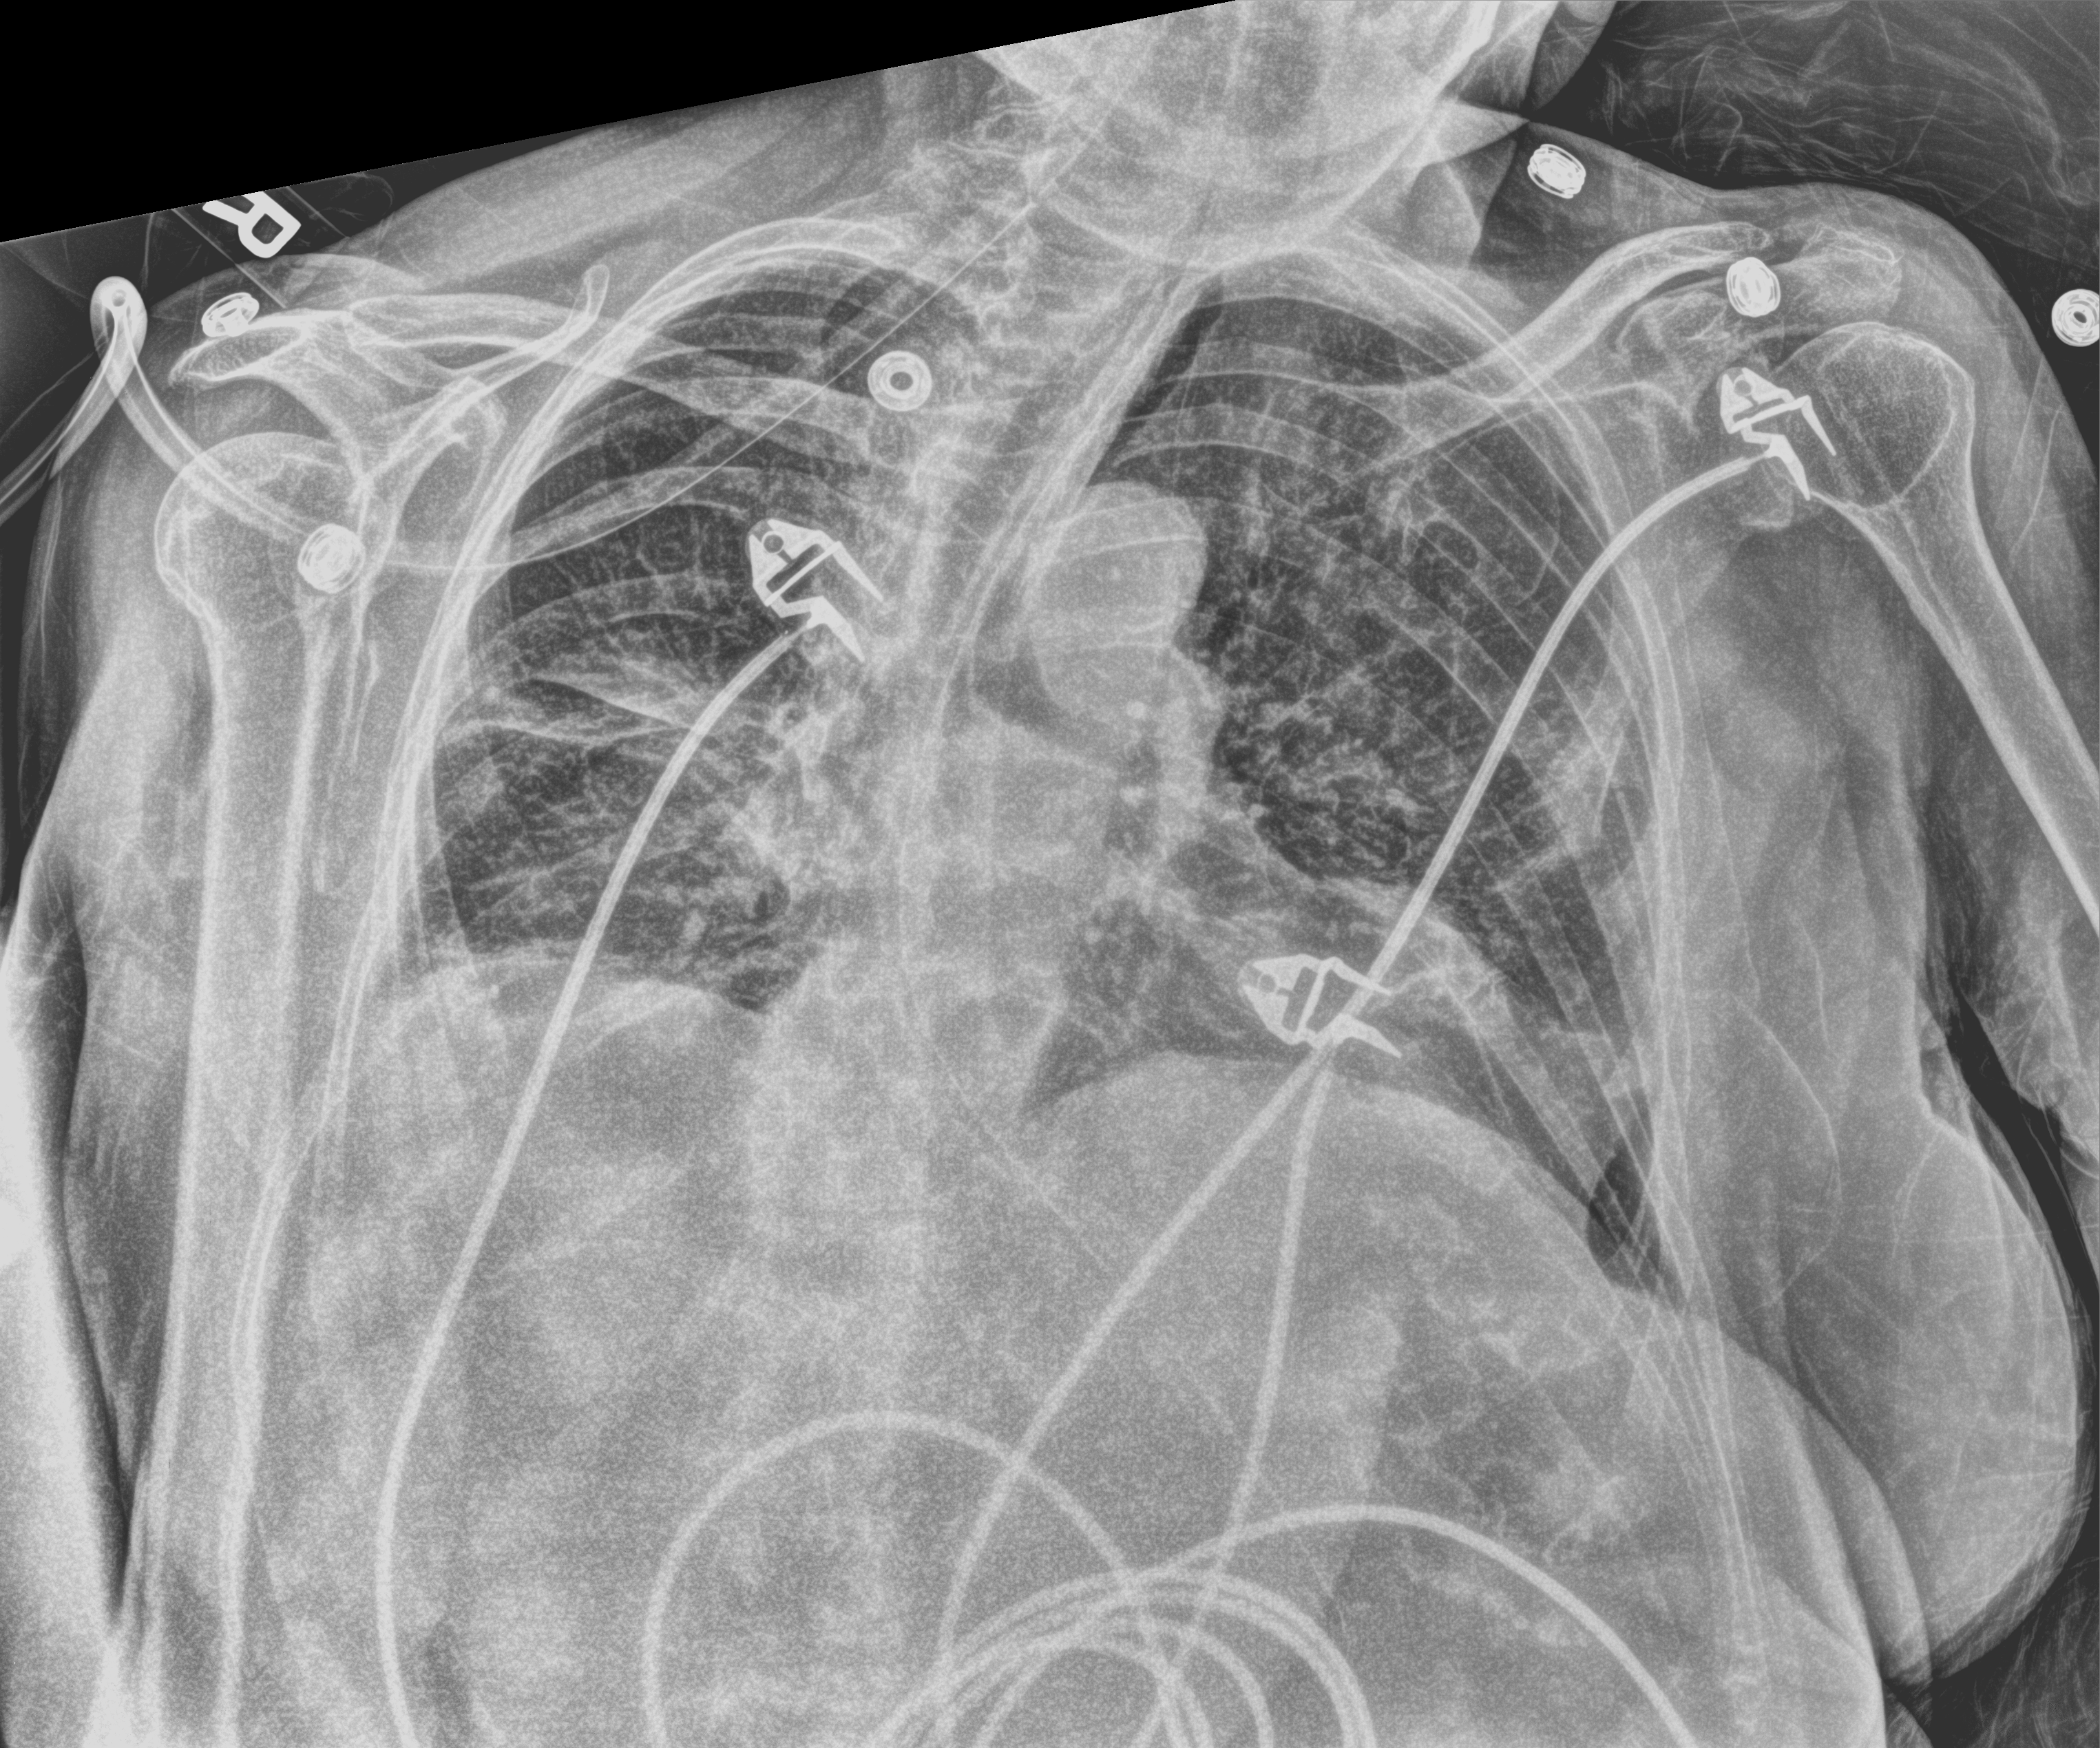
Chest X-ray (portable); anteroposterior (AP) projection. Patient hospitalised with COVID-19; female, aged 75–90 years.
Hospital-stay facts (about this admission, not read from this image; timing relative to this image not recorded): COPD (admission record): no; other chronic lung disease (admission record): yes; admitted to intensive care during this hospital stay: yes.